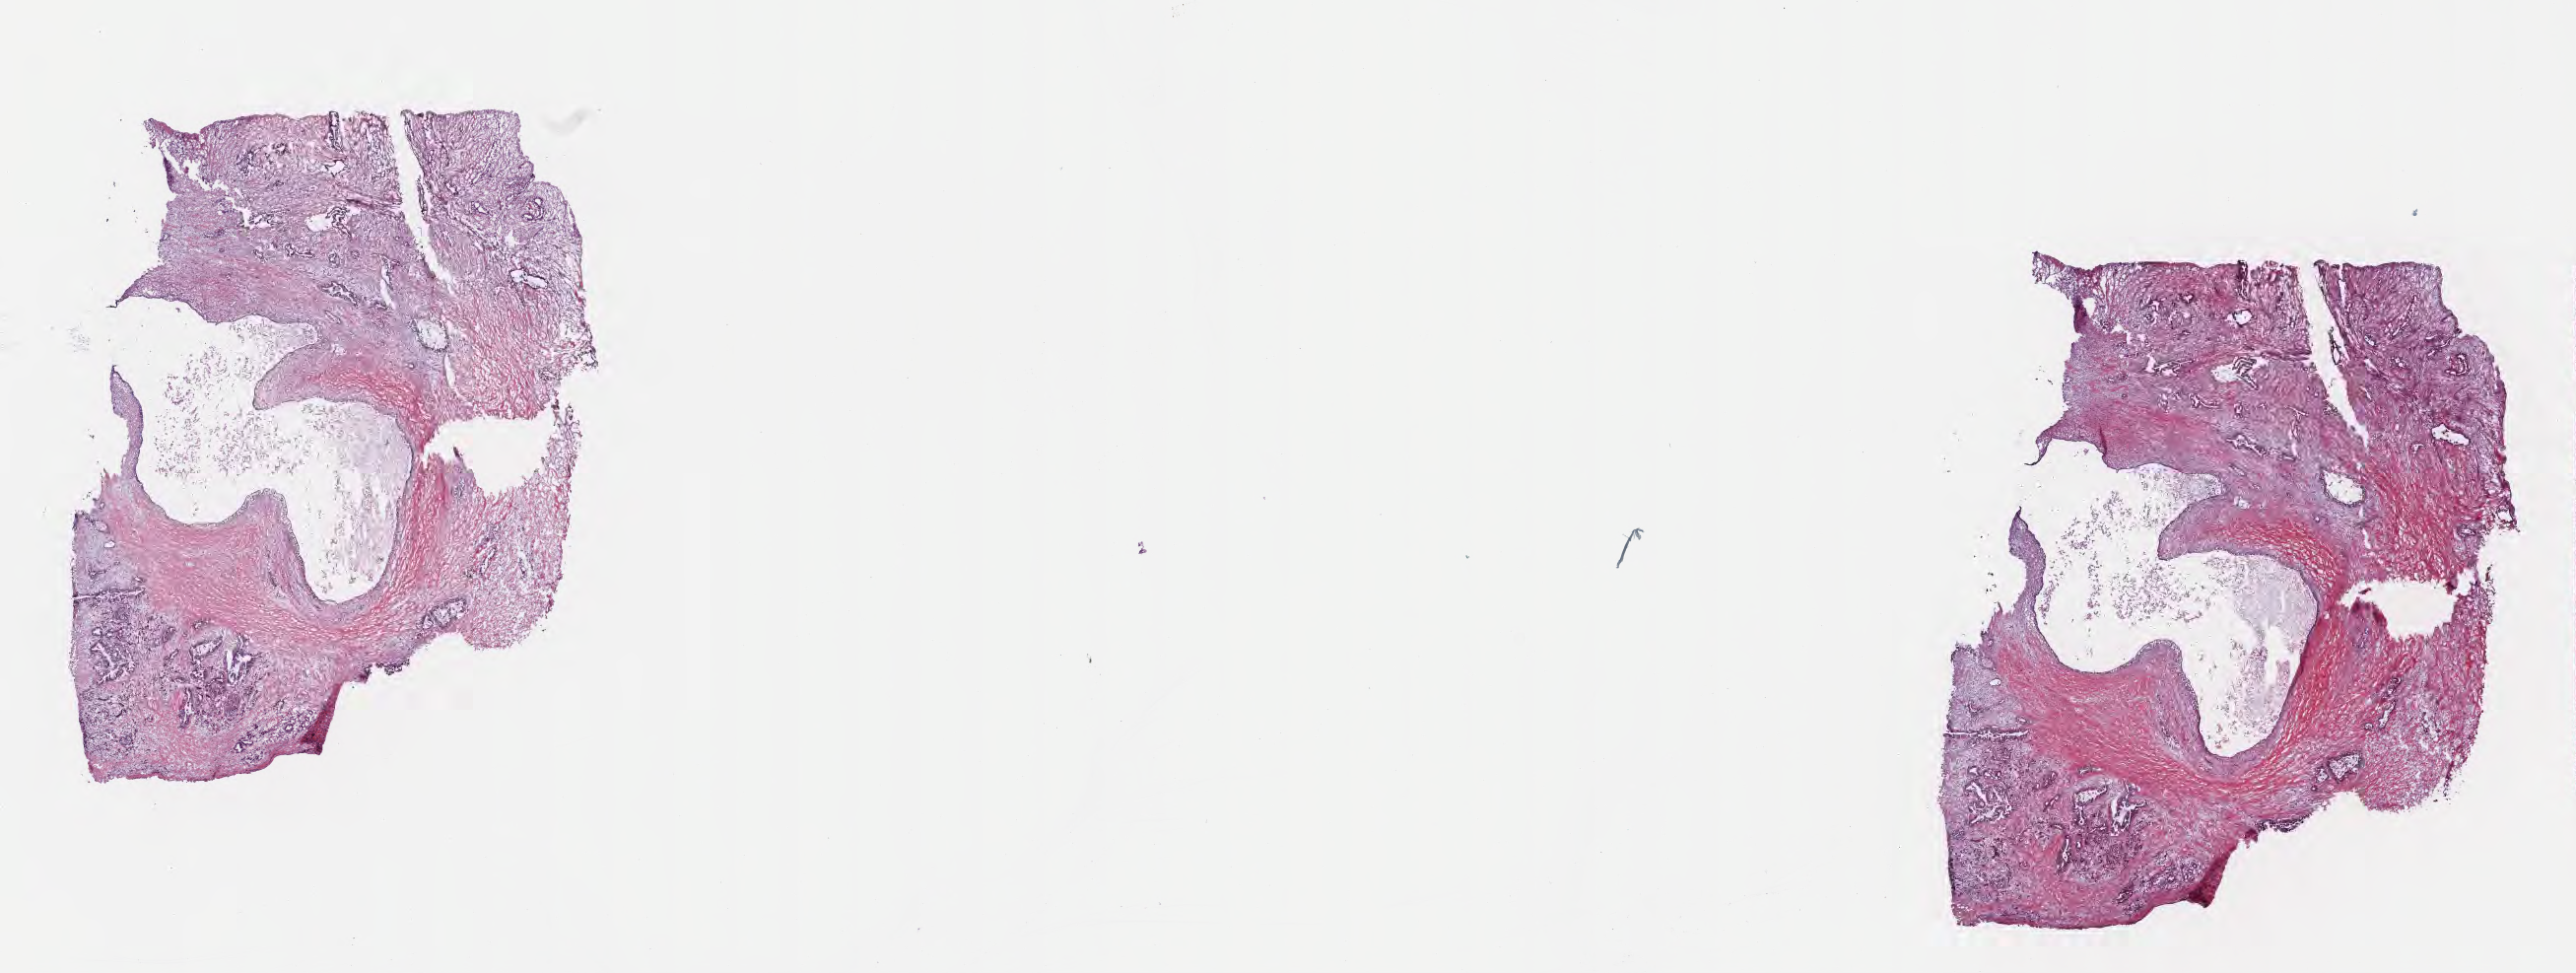
Digitized haematoxylin and eosin-stained section, whole scanned area (about 21.1 x 8.0 mm) shown as a low-resolution overview, frozen section (tissue freezing medium), primary tumor, site: head of pancreas. Patient: female, age at initial diagnosis 74 years. Tumor grade: G2 (moderately differentiated). Composition of this section per pathologist review: tumor cells 30%, tumor nuclei 30%, stromal cells 55%, necrosis 0%, normal cells 15%. Inflammatory infiltration, as recorded: lymphocyte infiltration 8%, monocyte infiltration 2%, neutrophil infiltration 0%.
- AJCC pathologic stage: Stage III
- diagnosis: Infiltrating duct carcinoma, NOS